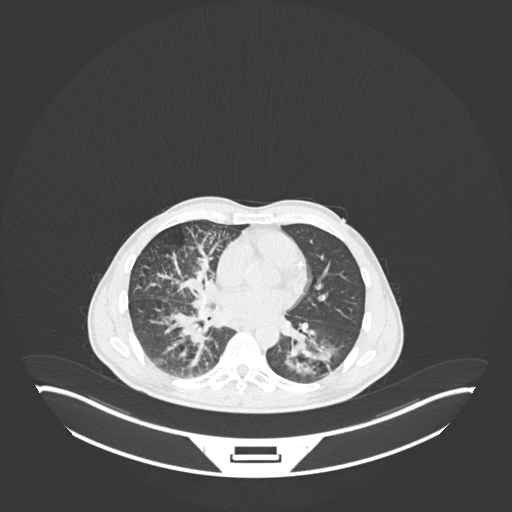
Chest CT, one axial slice. Slice 109 of 237 in the series (ordered by position). Lung window (W 1500 / L -600 HU). 1 mm slice thickness. 512 × 512 image matrix. Male patient, age 49 years. Case-level facts recorded for this patient, not image findings: clinical TNM (as recorded): T2b N1 M0.
Outlined on this slice (bounding box drawn by a radiologist):
- lung tumour (recorded histology: adenocarcinoma): bounding box <281,326,341,379> (left, top, right, bottom; pixels)